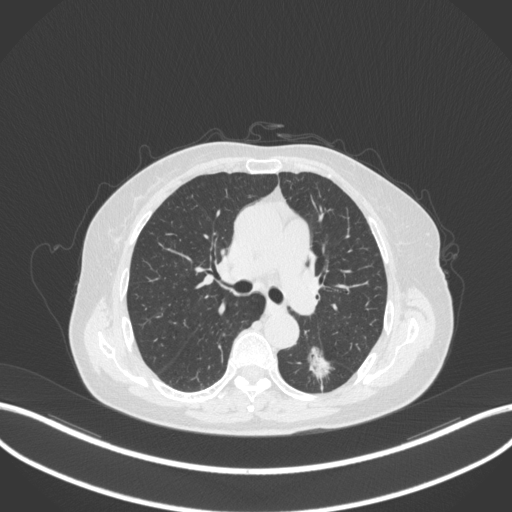
Chest CT, one axial slice. Position 183 of 352 along the scan axis. Reconstruction kernel B31f. Lung window (W 1500 / L -600 HU). 1 mm slice thickness. 512 × 512 image matrix, field of view 400 × 400 mm. Patient: female, 70 years. From the clinical record (not read from this slice): clinical TNM (as recorded): T1c N0 M0.
Annotated regions visible in this slice (bounding box drawn by a radiologist):
- lung tumour (recorded histology: adenocarcinoma): bounding box <301,338,339,381> (left, top, right, bottom; pixels)